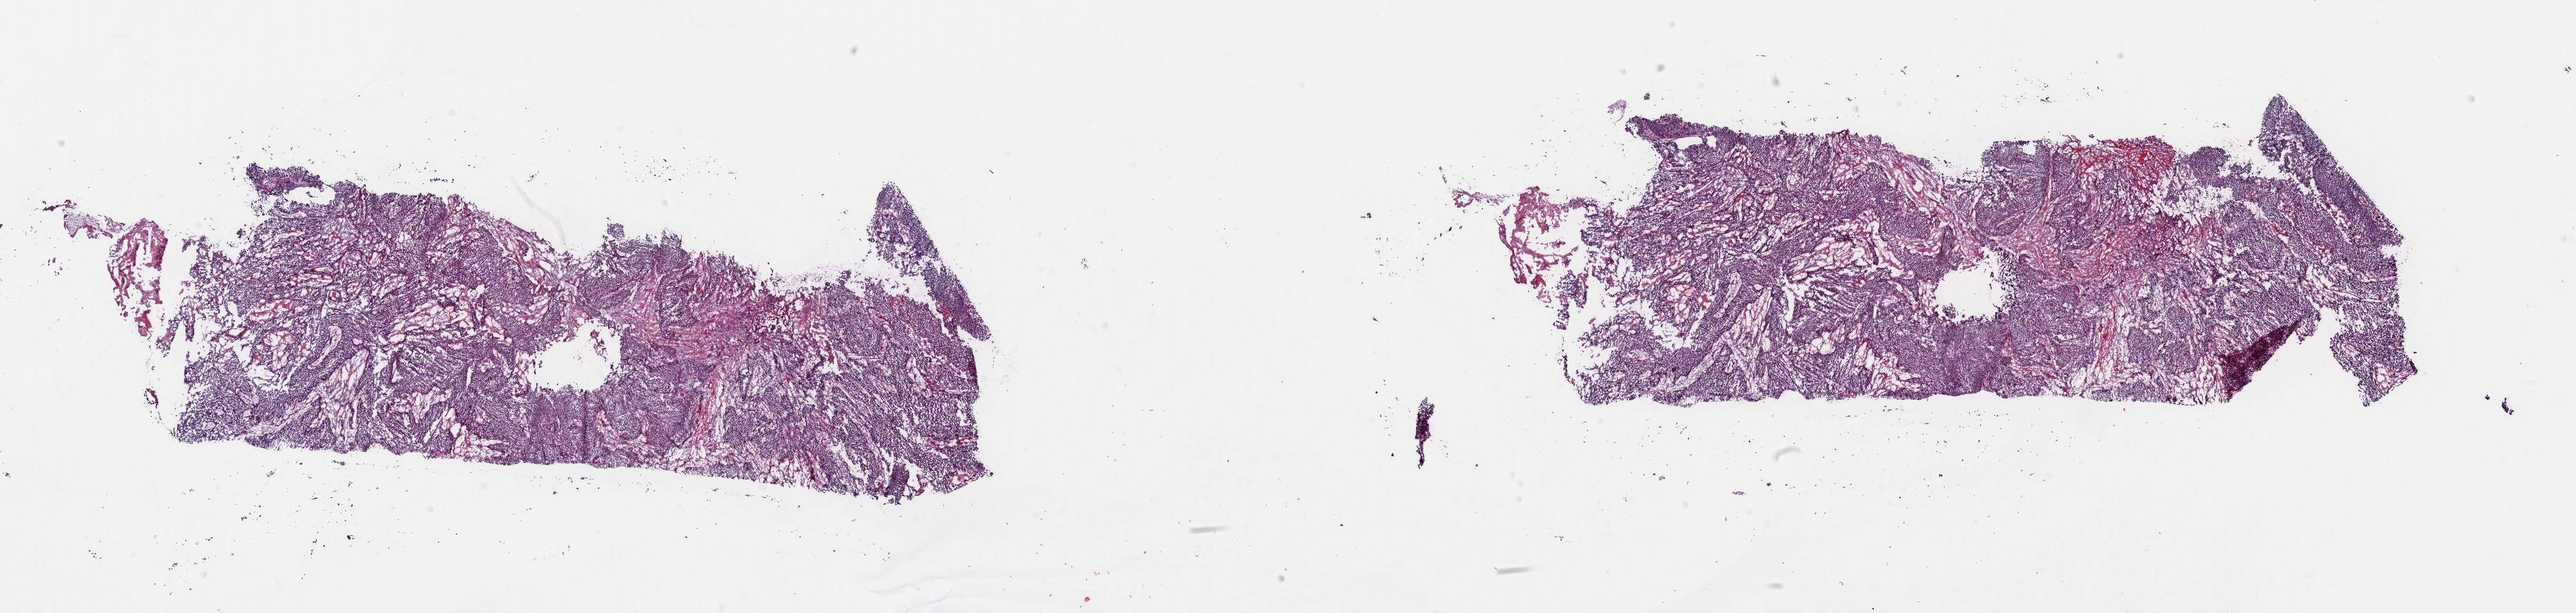
Whole-slide histology image, H&E-stained, shown as a low-resolution overview of the whole scanned area (about 32.0 x 7.6 mm), frozen section from the top of the tissue portion, sample: primary tumour, bladder. Male, age 70 years at initial diagnosis. Histologic grade: low grade. Composition of this section per pathologist review: tumour cells 80%, tumour nuclei 90%, normal cells 0%, stromal cells 20%, necrosis 0%. Infiltration values recorded for this section: lymphocyte infiltration 0%, monocyte infiltration 0%, neutrophil infiltration 0%.
Pathologic diagnosis: Transitional cell carcinoma (lateral wall of bladder). AJCC pathologic stage: II. TNM: T2 NX M0.